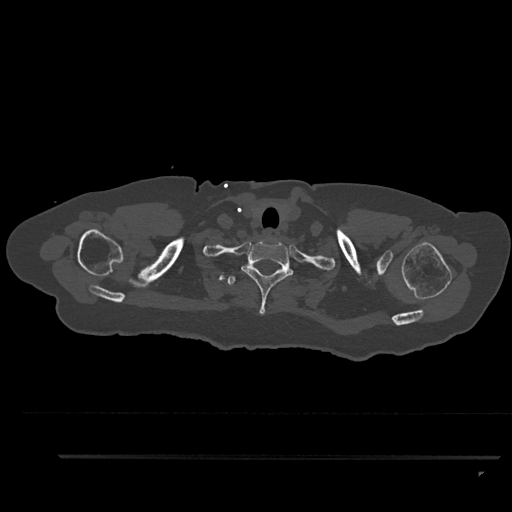
CT including the spine, one axial slice; slice 759 of 797 in the series (ordered by position); 120 kVp; bone window (W 1800 / L 400 HU); 0.5 mm slice thickness; 512 × 512 image matrix, field of view 408 × 408 mm. Patient: female, 44 years. From the clinical record (not read from this slice): primary cancer: renal.
Outlined on this slice (semi-automatic segmentation, software-assisted and operator-edited):
- T1 vertebra: bounding box (x1, y1, x2, y2) in pixels: (241, 240, 294, 315)
- T2 vertebra: (227, 276, 235, 285)